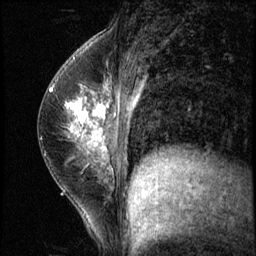
Breast MRI (dynamic contrast-enhanced), one sagittal slice. 3 images stored at this slice position (order not interpretable as contrast timing). 1.5 T. TE 4.2 ms, TR 8.7 ms. 256 × 256 image matrix, field of view 180 × 180 mm. Patient: female, 35 years. From the clinical record (not read from this slice): setting: breast cancer imaged before/during neoadjuvant chemotherapy; receptor status: HER2-positive.
Annotated regions visible in this slice (semi-automatic segmentation, software-assisted and operator-edited):
- analysis volume of interest (the breast-tissue region the enhancement analysis was run in; not a lesion): bounding box <58,84,138,186> (left, top, right, bottom; pixels)
- tumour enhancement mask (voxels above the 140 % enhancement threshold inside the analysis volume of interest): <64,87,110,151>